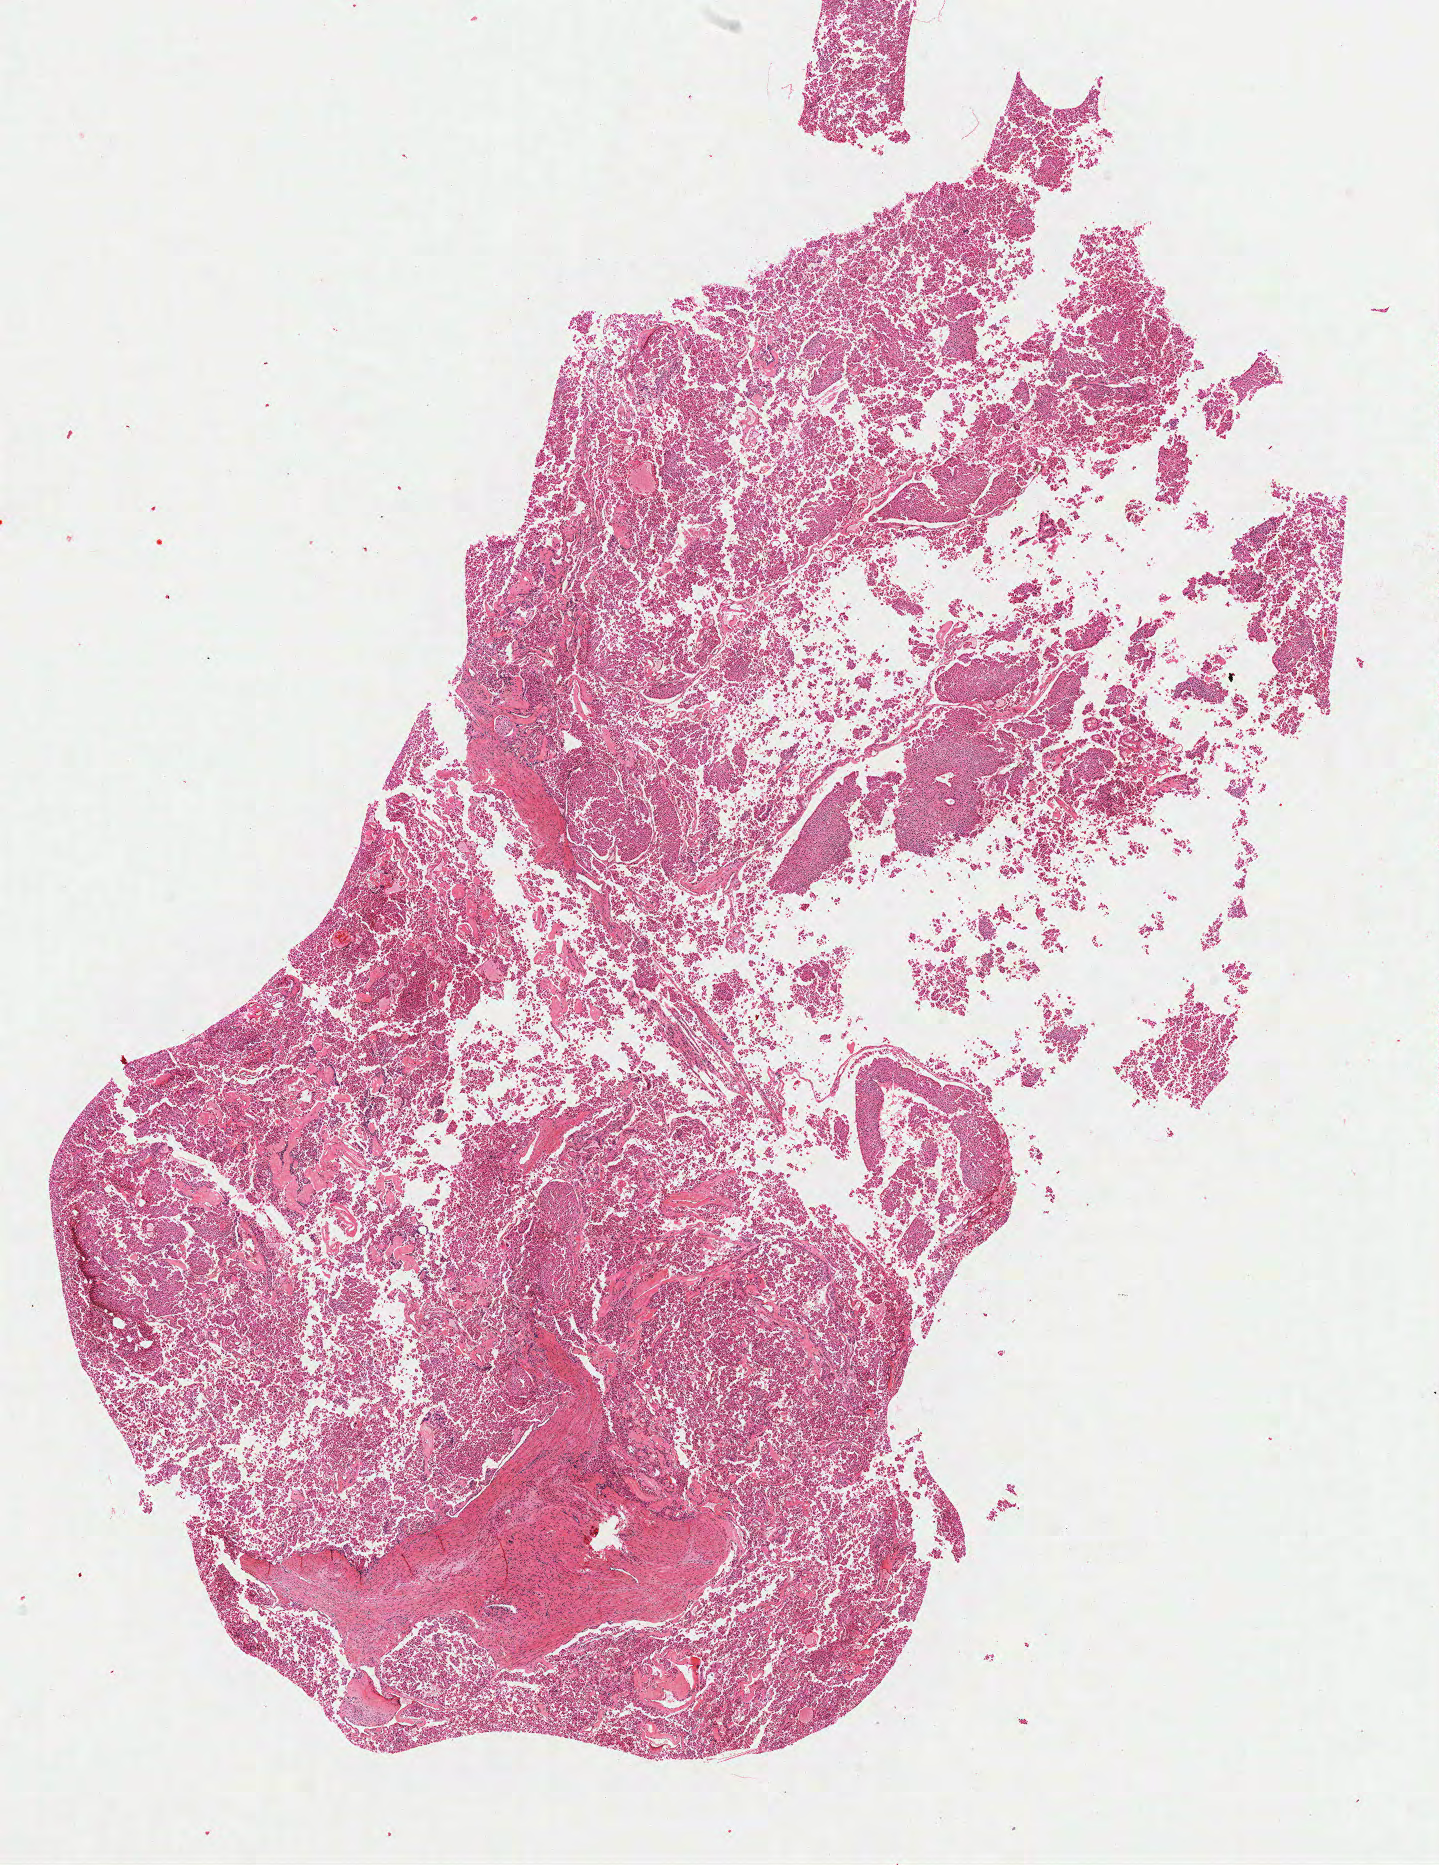
Hematoxylin and eosin (H&E) stained whole-slide image, a low-resolution overview of the entire scanned area, about 11.4 x 14.8 mm; formalin-fixed paraffin-embedded (FFPE) diagnostic section; sample: primary tumour, kidney. Female patient; age at initial diagnosis 71 years. Histologic grade: GX (grade cannot be assessed).
AJCC pathologic stage: I. Diagnosis: Clear cell adenocarcinoma, NOS.